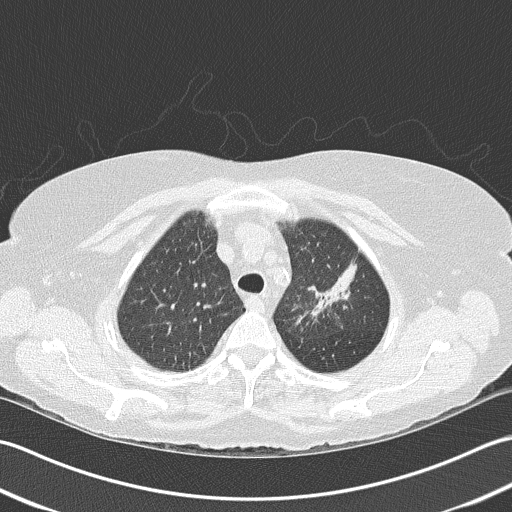
Axial slice from a low-dose chest CT screening exam; baseline annual screen; lung window (W 1500 / L -600 HU); 2 mm slice thickness; slice 128 of 159 in the series. Female participant, aged 68 years at enrolment.
Expert reader's lesion annotation, bounding box (x1, y1, x2, y2) in pixels: (294, 245, 368, 322). Screening reader's record for this exam: no non-calcified nodule ≥4 mm recorded. Official screen result: negative screen, minor abnormalities not suspicious for lung cancer. Later outcome: lung cancer diagnosed 763 days after this screen — adenocarcinoma, NOS, left upper lobe, poorly differentiated (G3), stage IB (AJCC 6th edition), 50 mm at pathology.